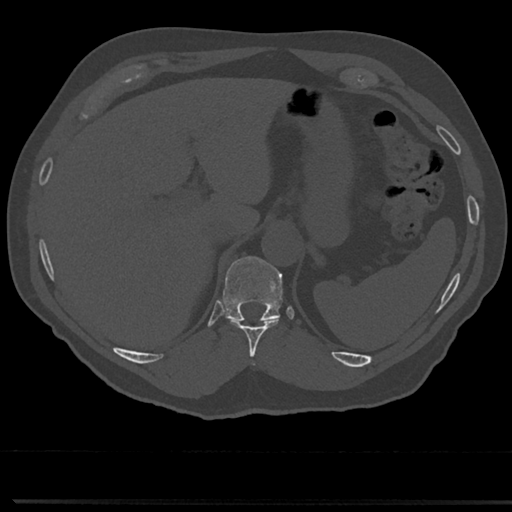
CT including the spine, one axial slice. Position 229 of 817 along the scan axis. 120 kVp. Bone window (W 1800 / L 400 HU). 0.5 mm slice thickness. 512 × 512 image matrix, field of view 355 × 355 mm. Patient: male, 61 years. From the clinical record (not read from this slice): primary cancer: prostate.
Structures marked on this image (semi-automatically segmented with operator editing):
- T10 vertebra: bounding box [x1, y1, x2, y2] px = [227, 317, 281, 354]
- T11 vertebra: [224, 256, 281, 322]